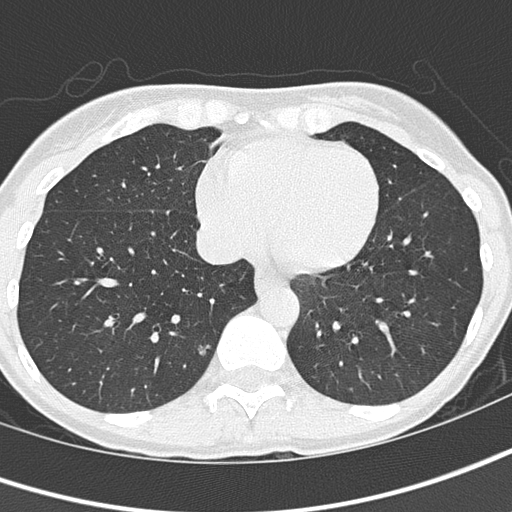
Low-dose screening chest CT, one axial slice; position 48 of 145 along the scan axis; reconstruction kernel B50f; 120 kVp; lung window (W 1500 / L -600 HU); 512 × 512 image matrix, field of view 276 × 276 mm.
Annotated regions visible in this slice (expert manual segmentation):
- lesion 1 (tumor, lower lobe of right lung): box from (x=200, y=345) to (x=209, y=354) px